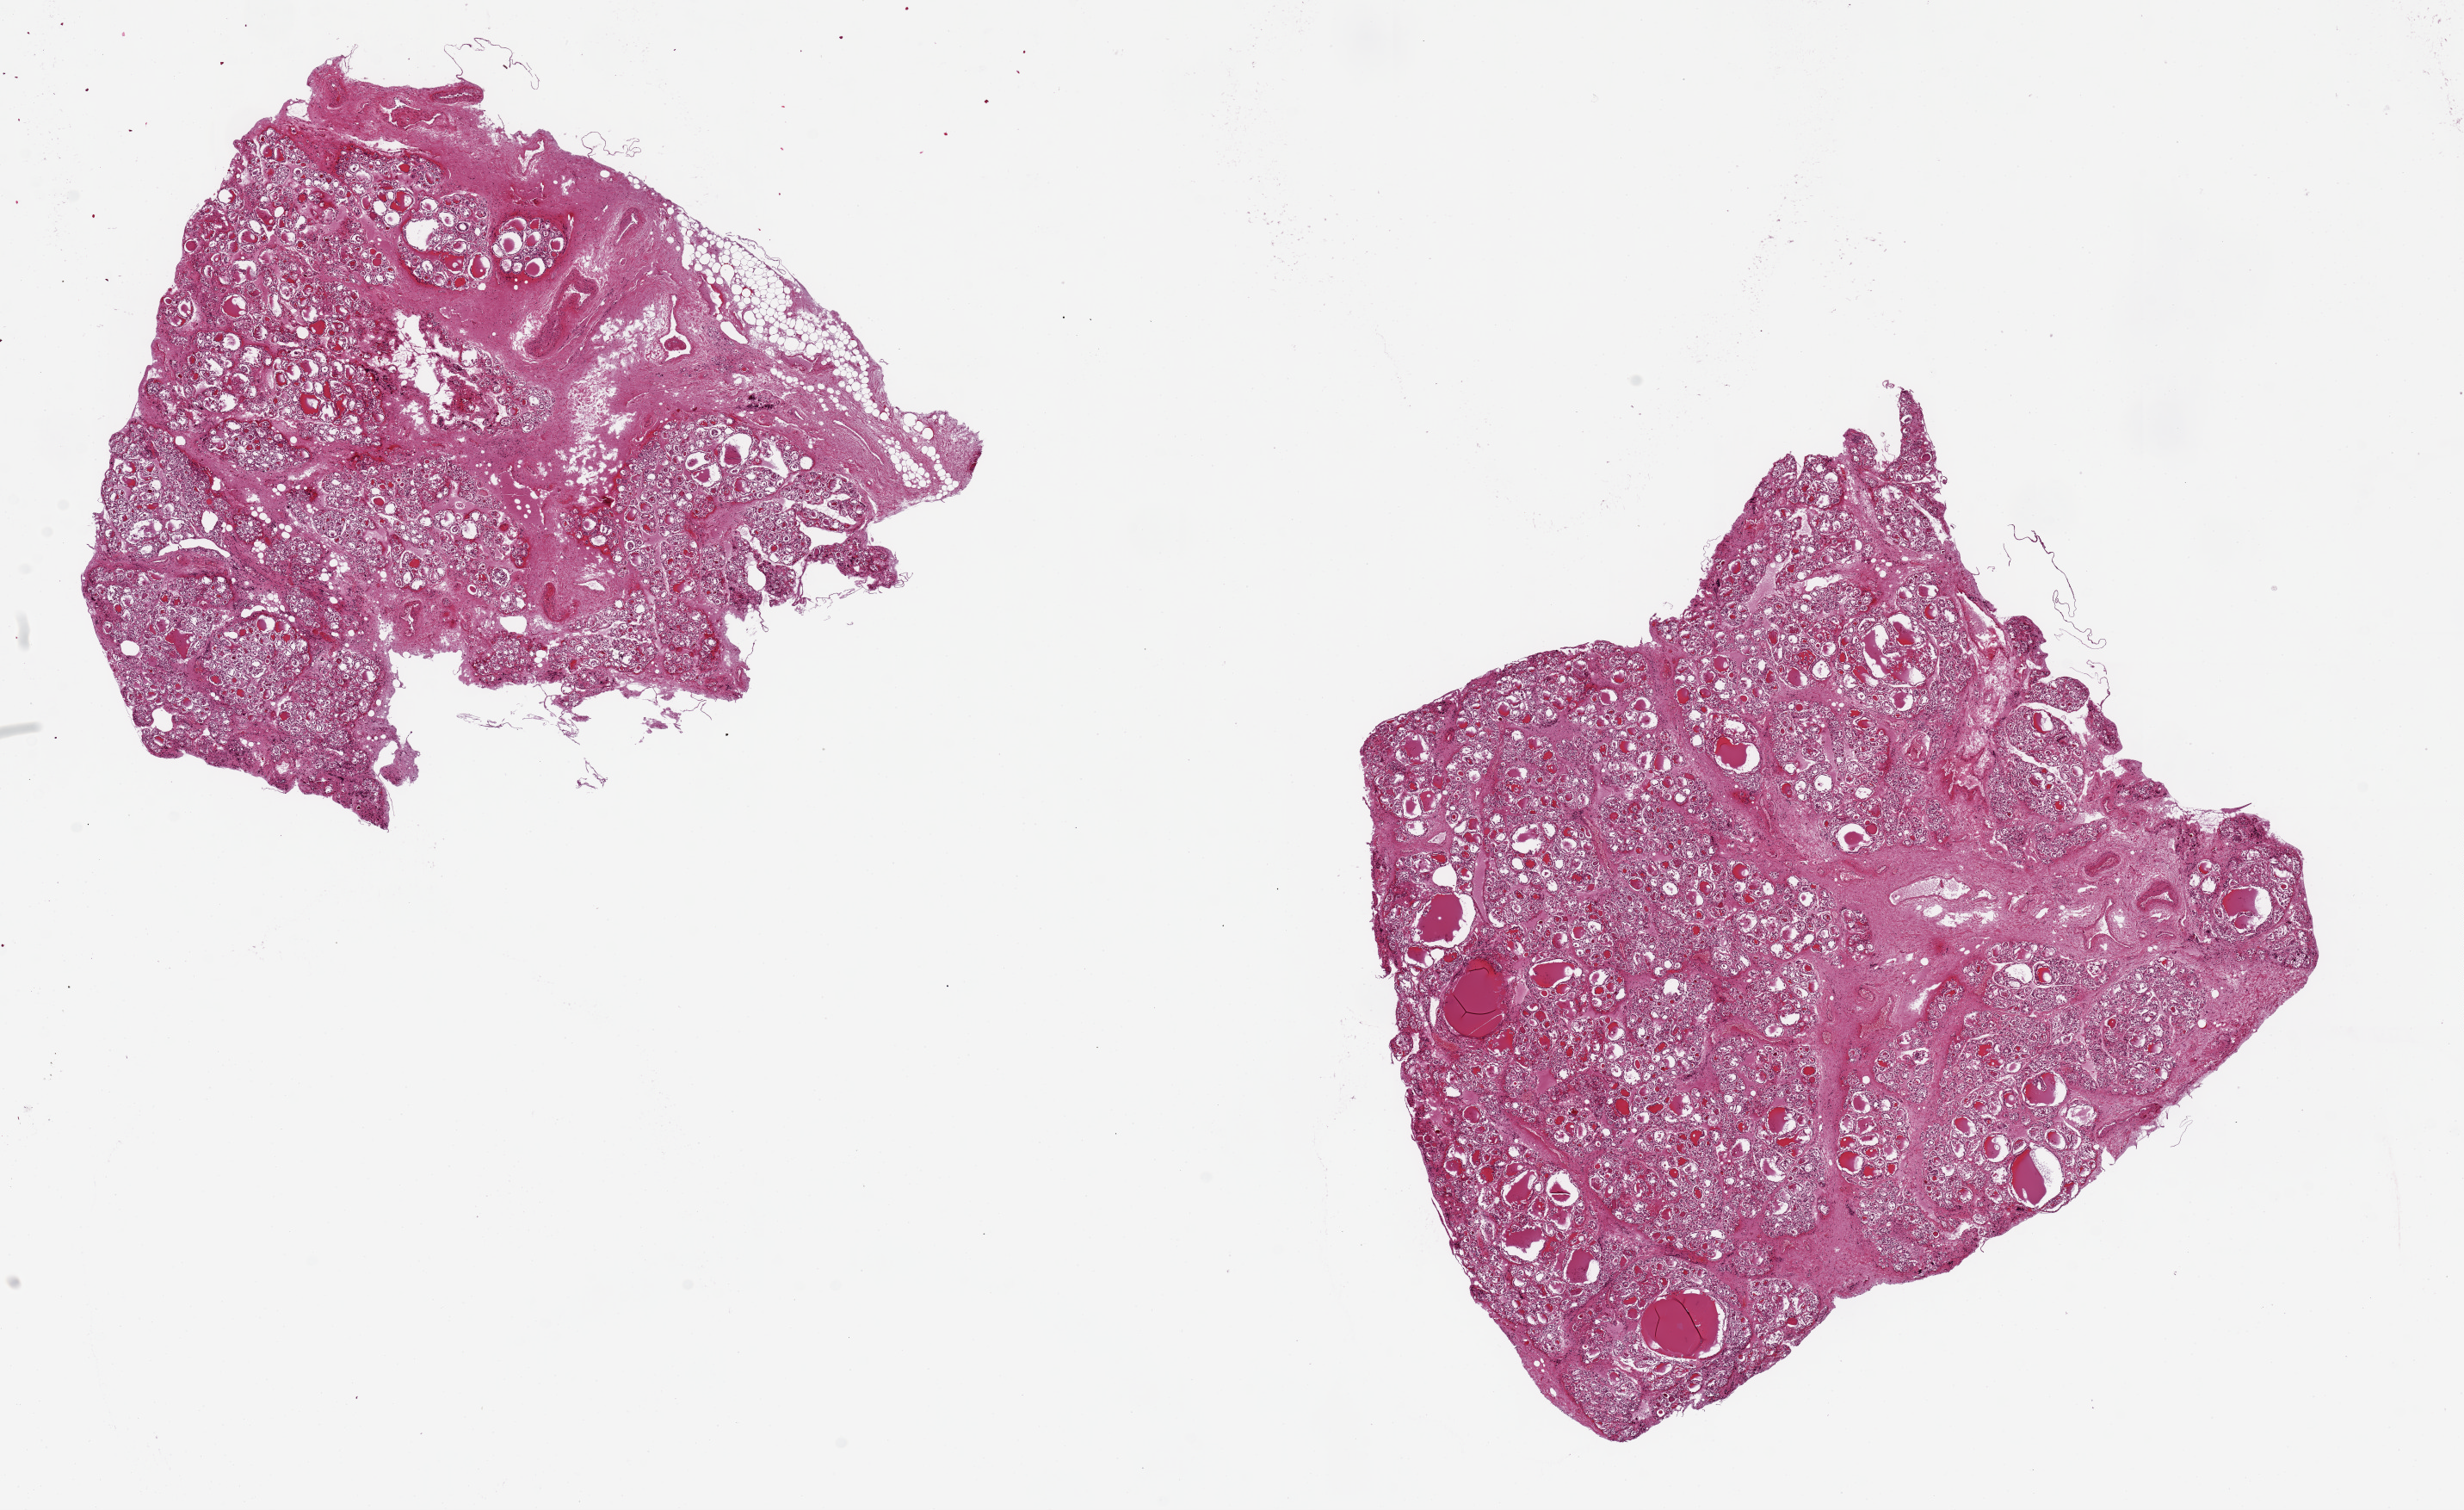
Haematoxylin and eosin whole-slide image — a low-resolution overview of the entire scanned area, about 22.6 x 13.9 mm. PAXgene-fixed, paraffin-embedded tissue. Sampled site (target tissue): thyroid. Tissue donor sample. Female donor.
Review note (as recorded): 2 pieces, 8x7 & 8.5x7mm; unusually badly autolyzed.